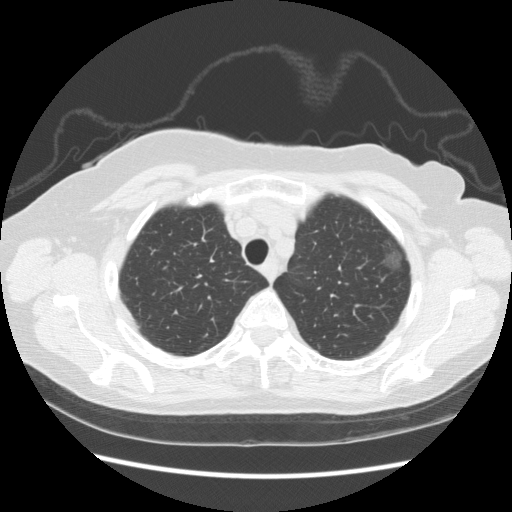
Low-dose screening chest CT, axial slice; baseline screening round; lung window (W 1500 / L -600 HU); standard (soft-tissue) reconstruction kernel (STANDARD); slice 34 of 247 in the series. Female participant, aged 73 years at enrolment. Former smoker at enrolment.
Lesion marked by an expert reader, bounding box <372,231,414,277> (left, top, right, bottom; pixels). The screening reader recorded 3 non-calcified nodules or masses ≥4 mm on this exam (left upper lobe, left upper lobe, left upper lobe); which of them this box marks is not recorded. Lung cancer was diagnosed 445 days after this screen (after the second annual screen): bronchiolo-alveolar adenocarcinoma, NOS, left upper lobe, well differentiated (G1), stage IA (AJCC 6th edition), 10 mm at pathology.